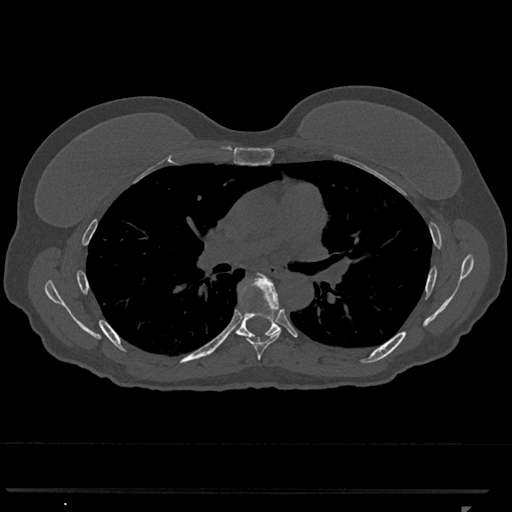
CT including the spine, one axial slice. 120 kVp. Bone window (W 1800 / L 400 HU). 0.5 mm slice thickness. 512 × 512 image matrix. Patient: female, 62 years. From the clinical record (not read from this slice): primary cancer: renal.
Outlined on this slice (semi-automatic segmentation, software-assisted and operator-edited):
- T6 vertebra: bounding box <238,275,281,360> (left, top, right, bottom; pixels)
- T7 vertebra: <226,288,280,346>